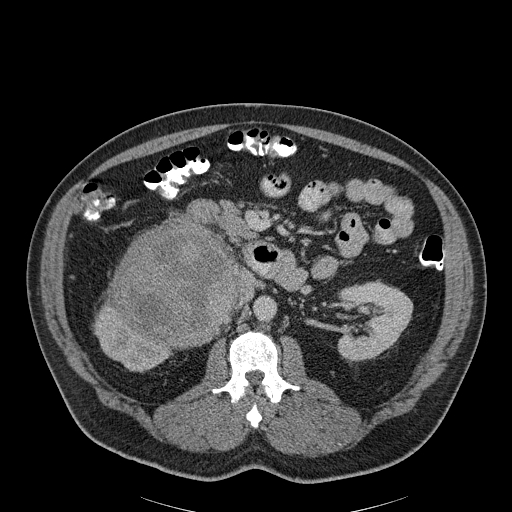
Contrast-enhanced abdominal CT, one axial slice; slice 112 of 186 in the series (ordered by position); reconstruction kernel B30f; 120 kVp; soft-tissue window (W 400 / L 40 HU); 512 × 512 image matrix, field of view 464 × 464 mm. Patient: male, 56 years. Case-level facts recorded for this patient, not image findings: diagnosis: adrenocortical carcinoma; tumour side: right adrenal; tumour size at pathology: 18 cm; Ki-67 index: 2 %; stage (as recorded): 3.
Outlined on this slice (semi-automatically segmented with operator editing):
- mass: box from (x=113, y=225) to (x=239, y=344) px